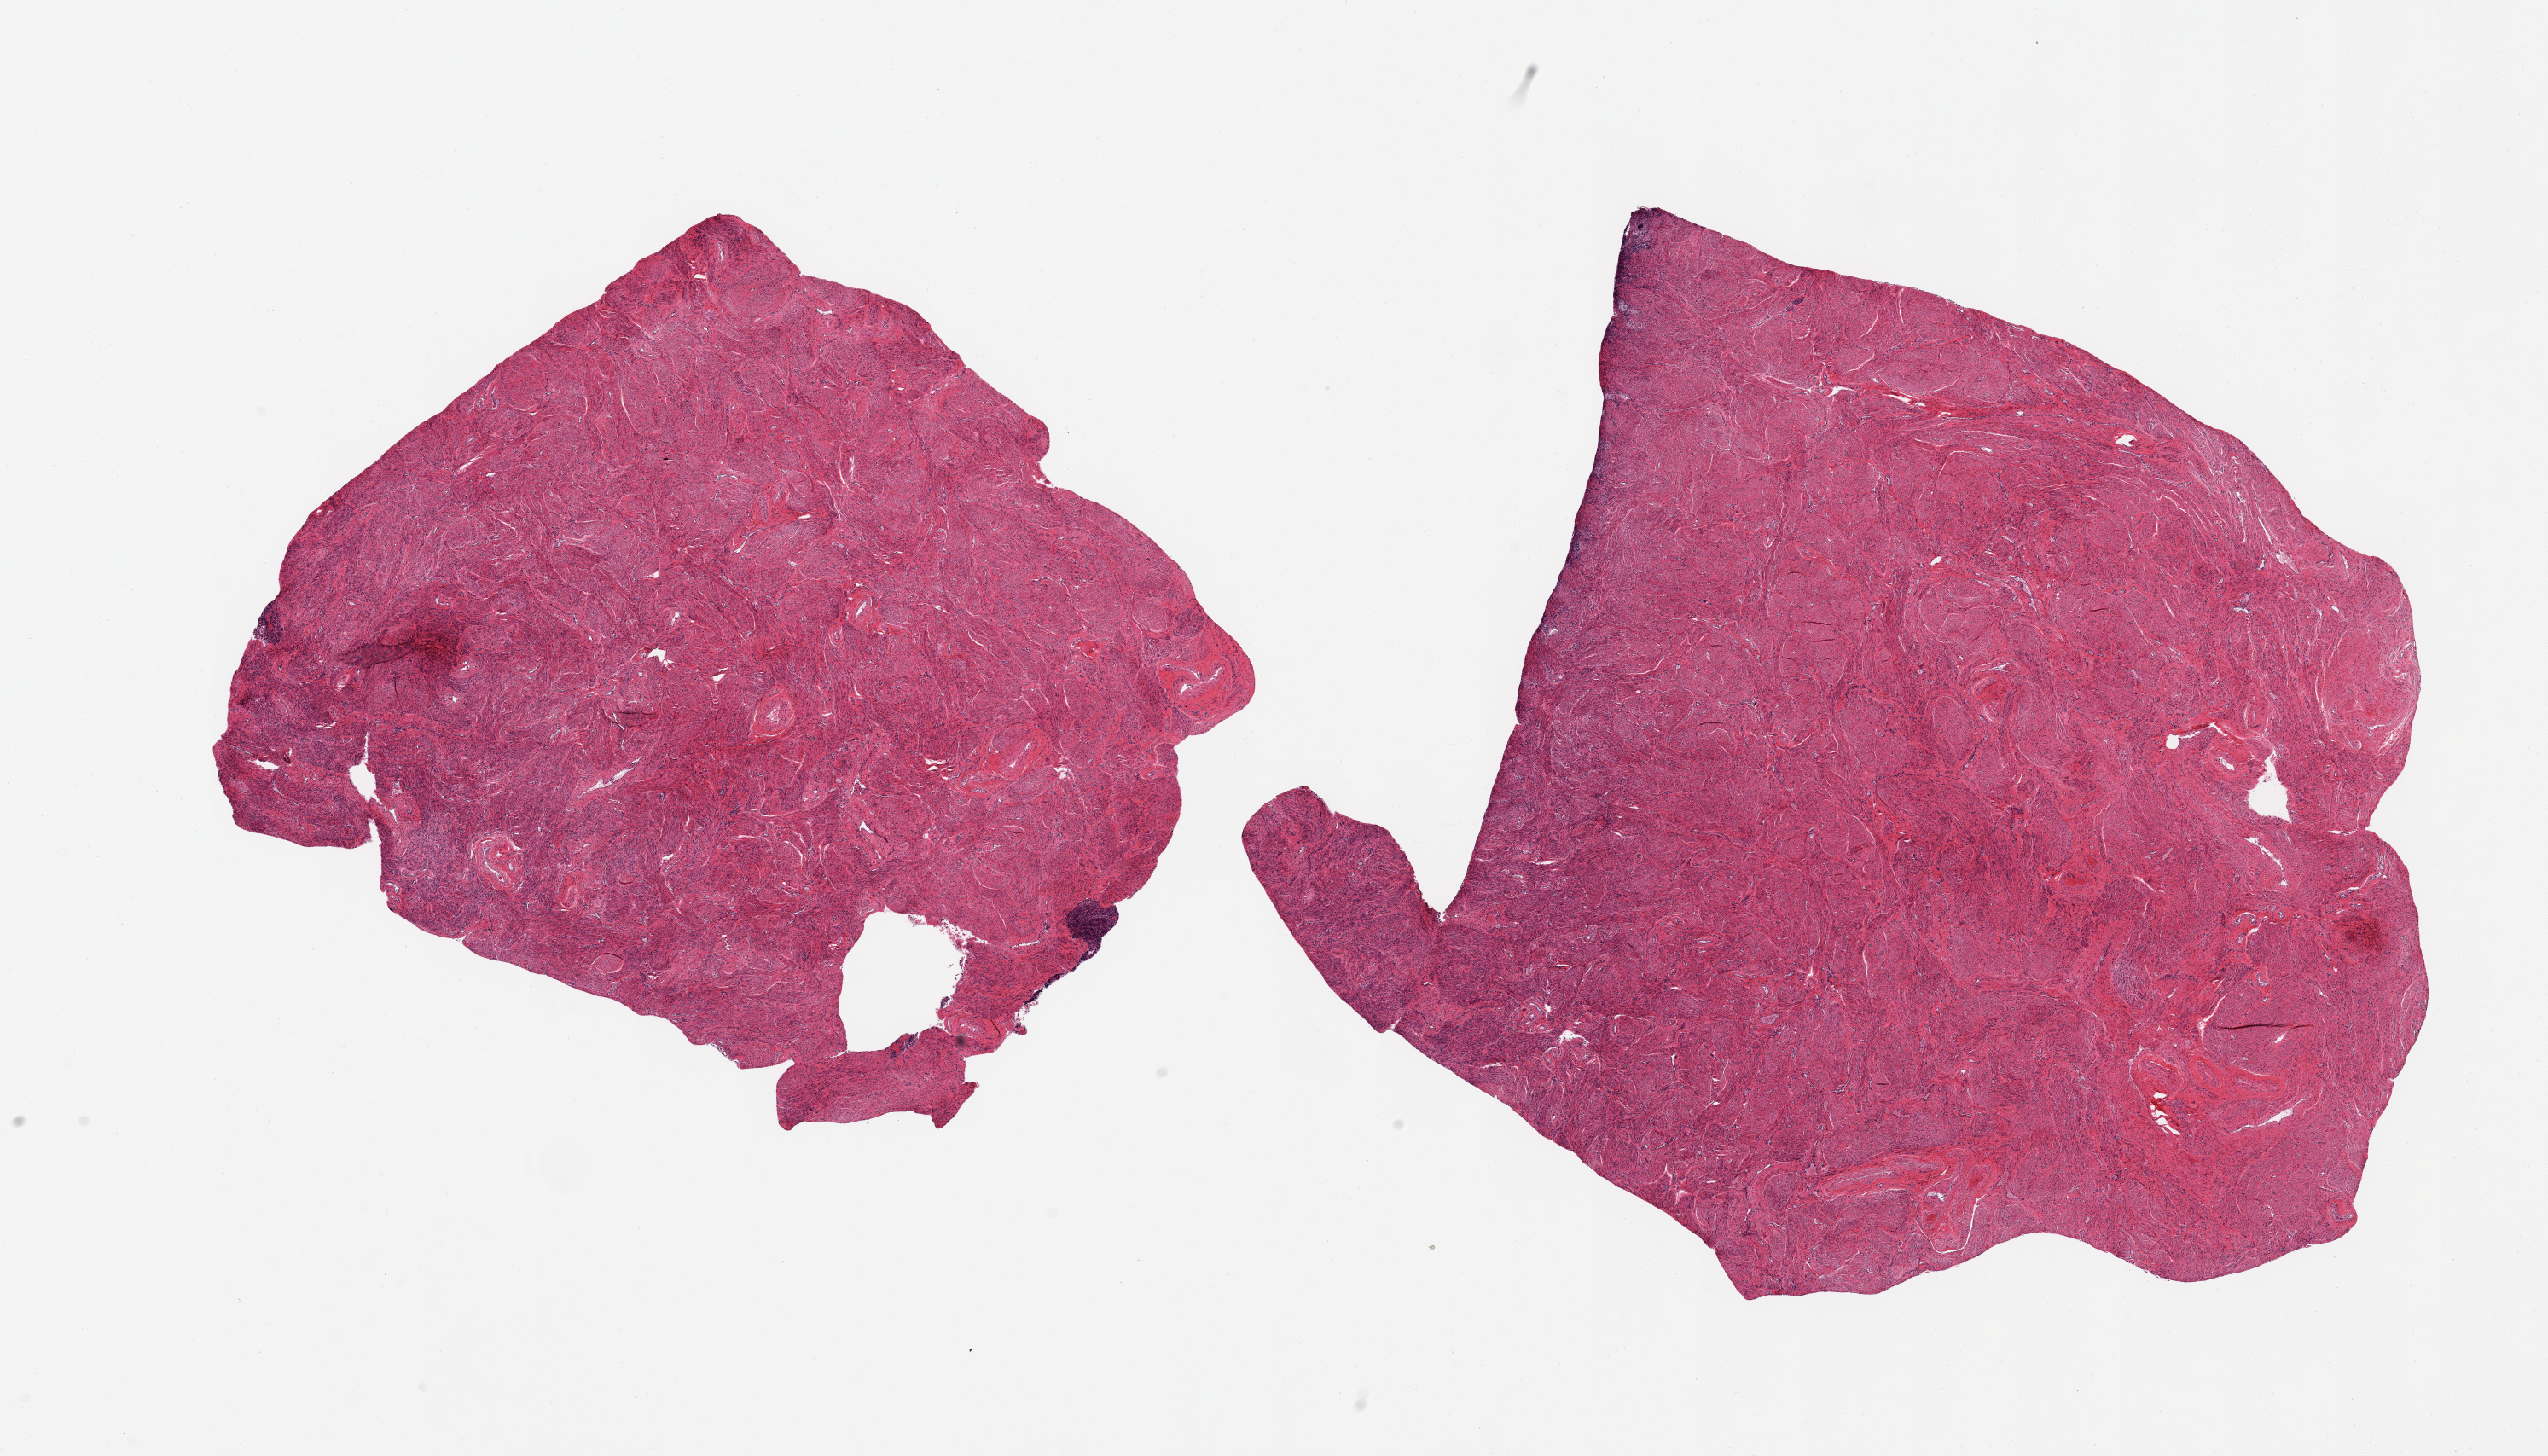
Whole-slide image, H&E stain, a low-resolution overview of the entire scanned area, about 23.6 x 13.5 mm, PAXgene-fixed, paraffin-embedded tissue, target tissue: uterus, tissue donor sample. Donor: female.
- review note (as recorded): 2 pieces, all myometrium